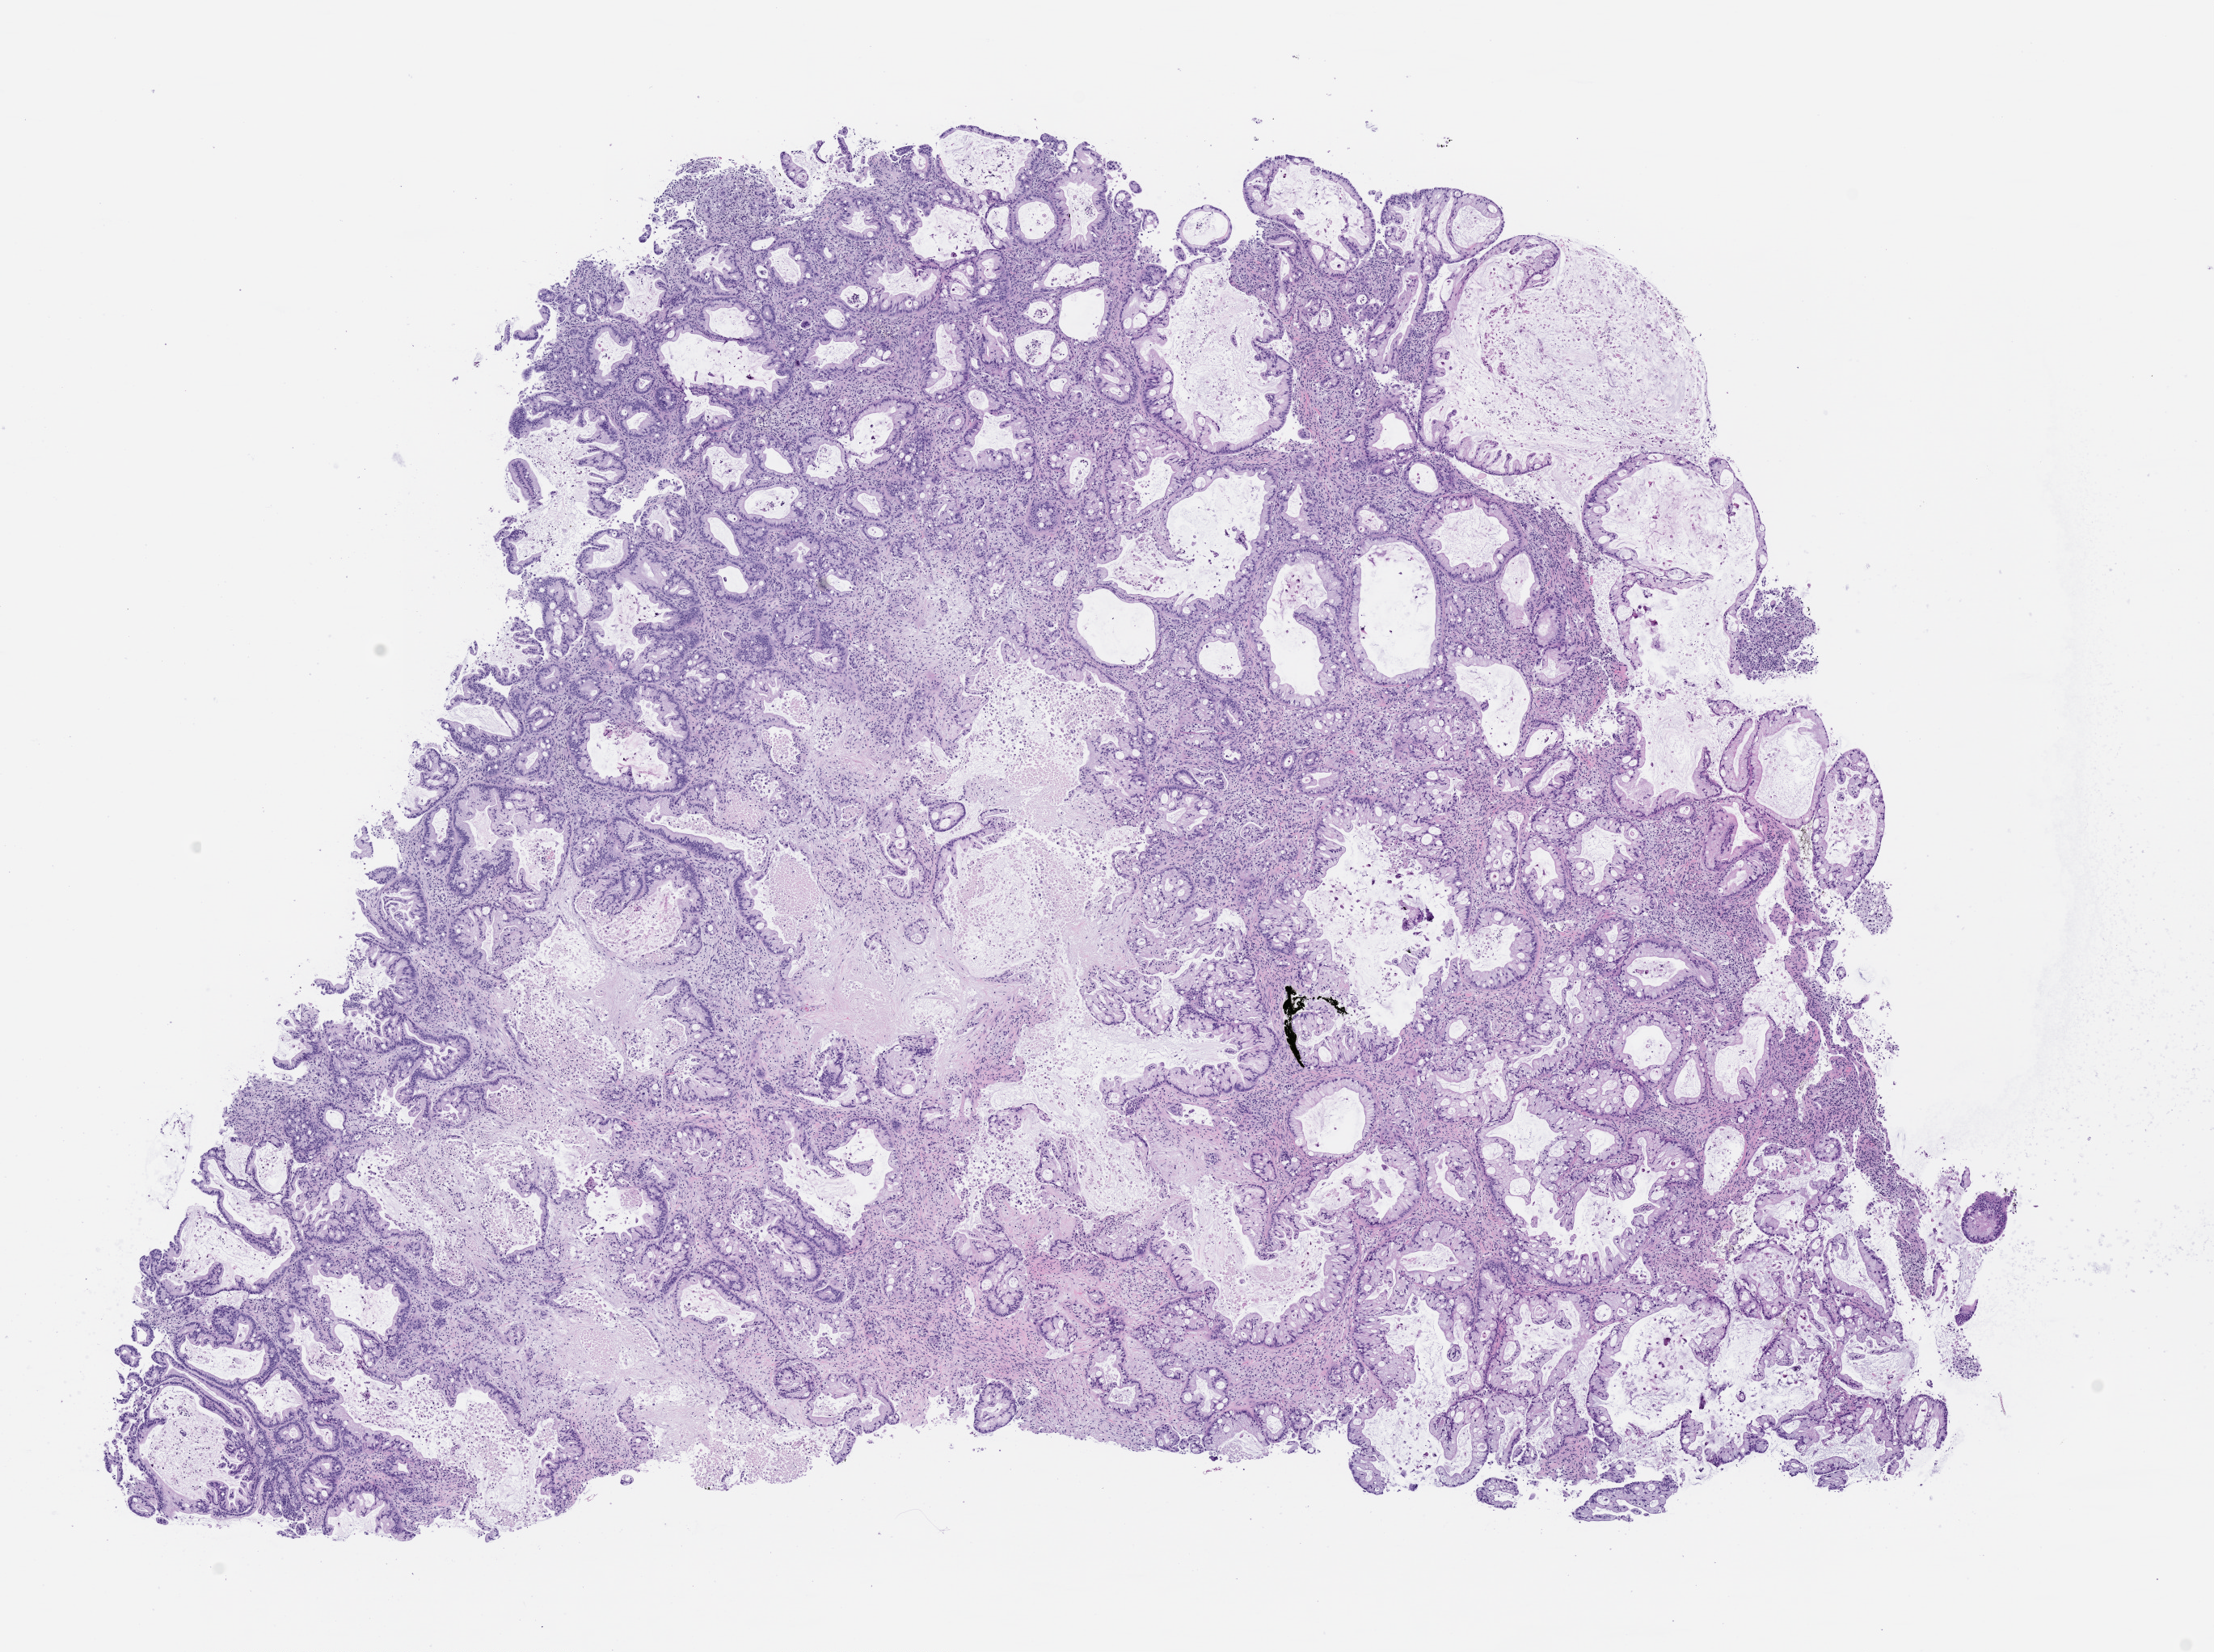
Whole-slide image, hematoxylin and eosin (H&E): patient-derived xenograft (human tumor grown in a mouse), passage 0 — a low-resolution overview of the entire scanned area, about 11.0 x 8.2 mm. FFPE section. Originating tumor site category: pancreas.
• originating patient diagnosis: Pancreatic Adenocarcinoma